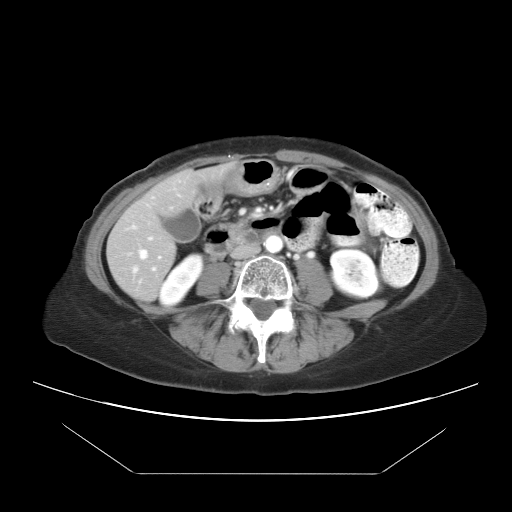
Contrast-enhanced abdominal CT, one axial slice; slice 4 of 21 in the series (ordered by position); reconstruction kernel STANDARD; 120 kVp; intravenous contrast given; soft-tissue window (W 400 / L 40 HU); 7.5 mm slice thickness; 512 × 512 image matrix, field of view 392 × 392 mm. Female patient, age 72 years. From the clinical record (not read from this slice): diagnosis: colorectal cancer liver metastases, imaged before liver resection; multiple liver metastases: yes; largest metastasis: 4 cm; disease in both lobes: yes.
Annotated regions visible in this slice (expert manual segmentation):
- hepatic veins: box from (x=132, y=248) to (x=149, y=274) px
- liver: (x=108, y=175)–(x=211, y=300)
- planned liver remnant (the part of the liver to remain after resection): (x=108, y=175)–(x=211, y=295)
- portal vein (with intrahepatic branches): (x=148, y=236)–(x=161, y=258)